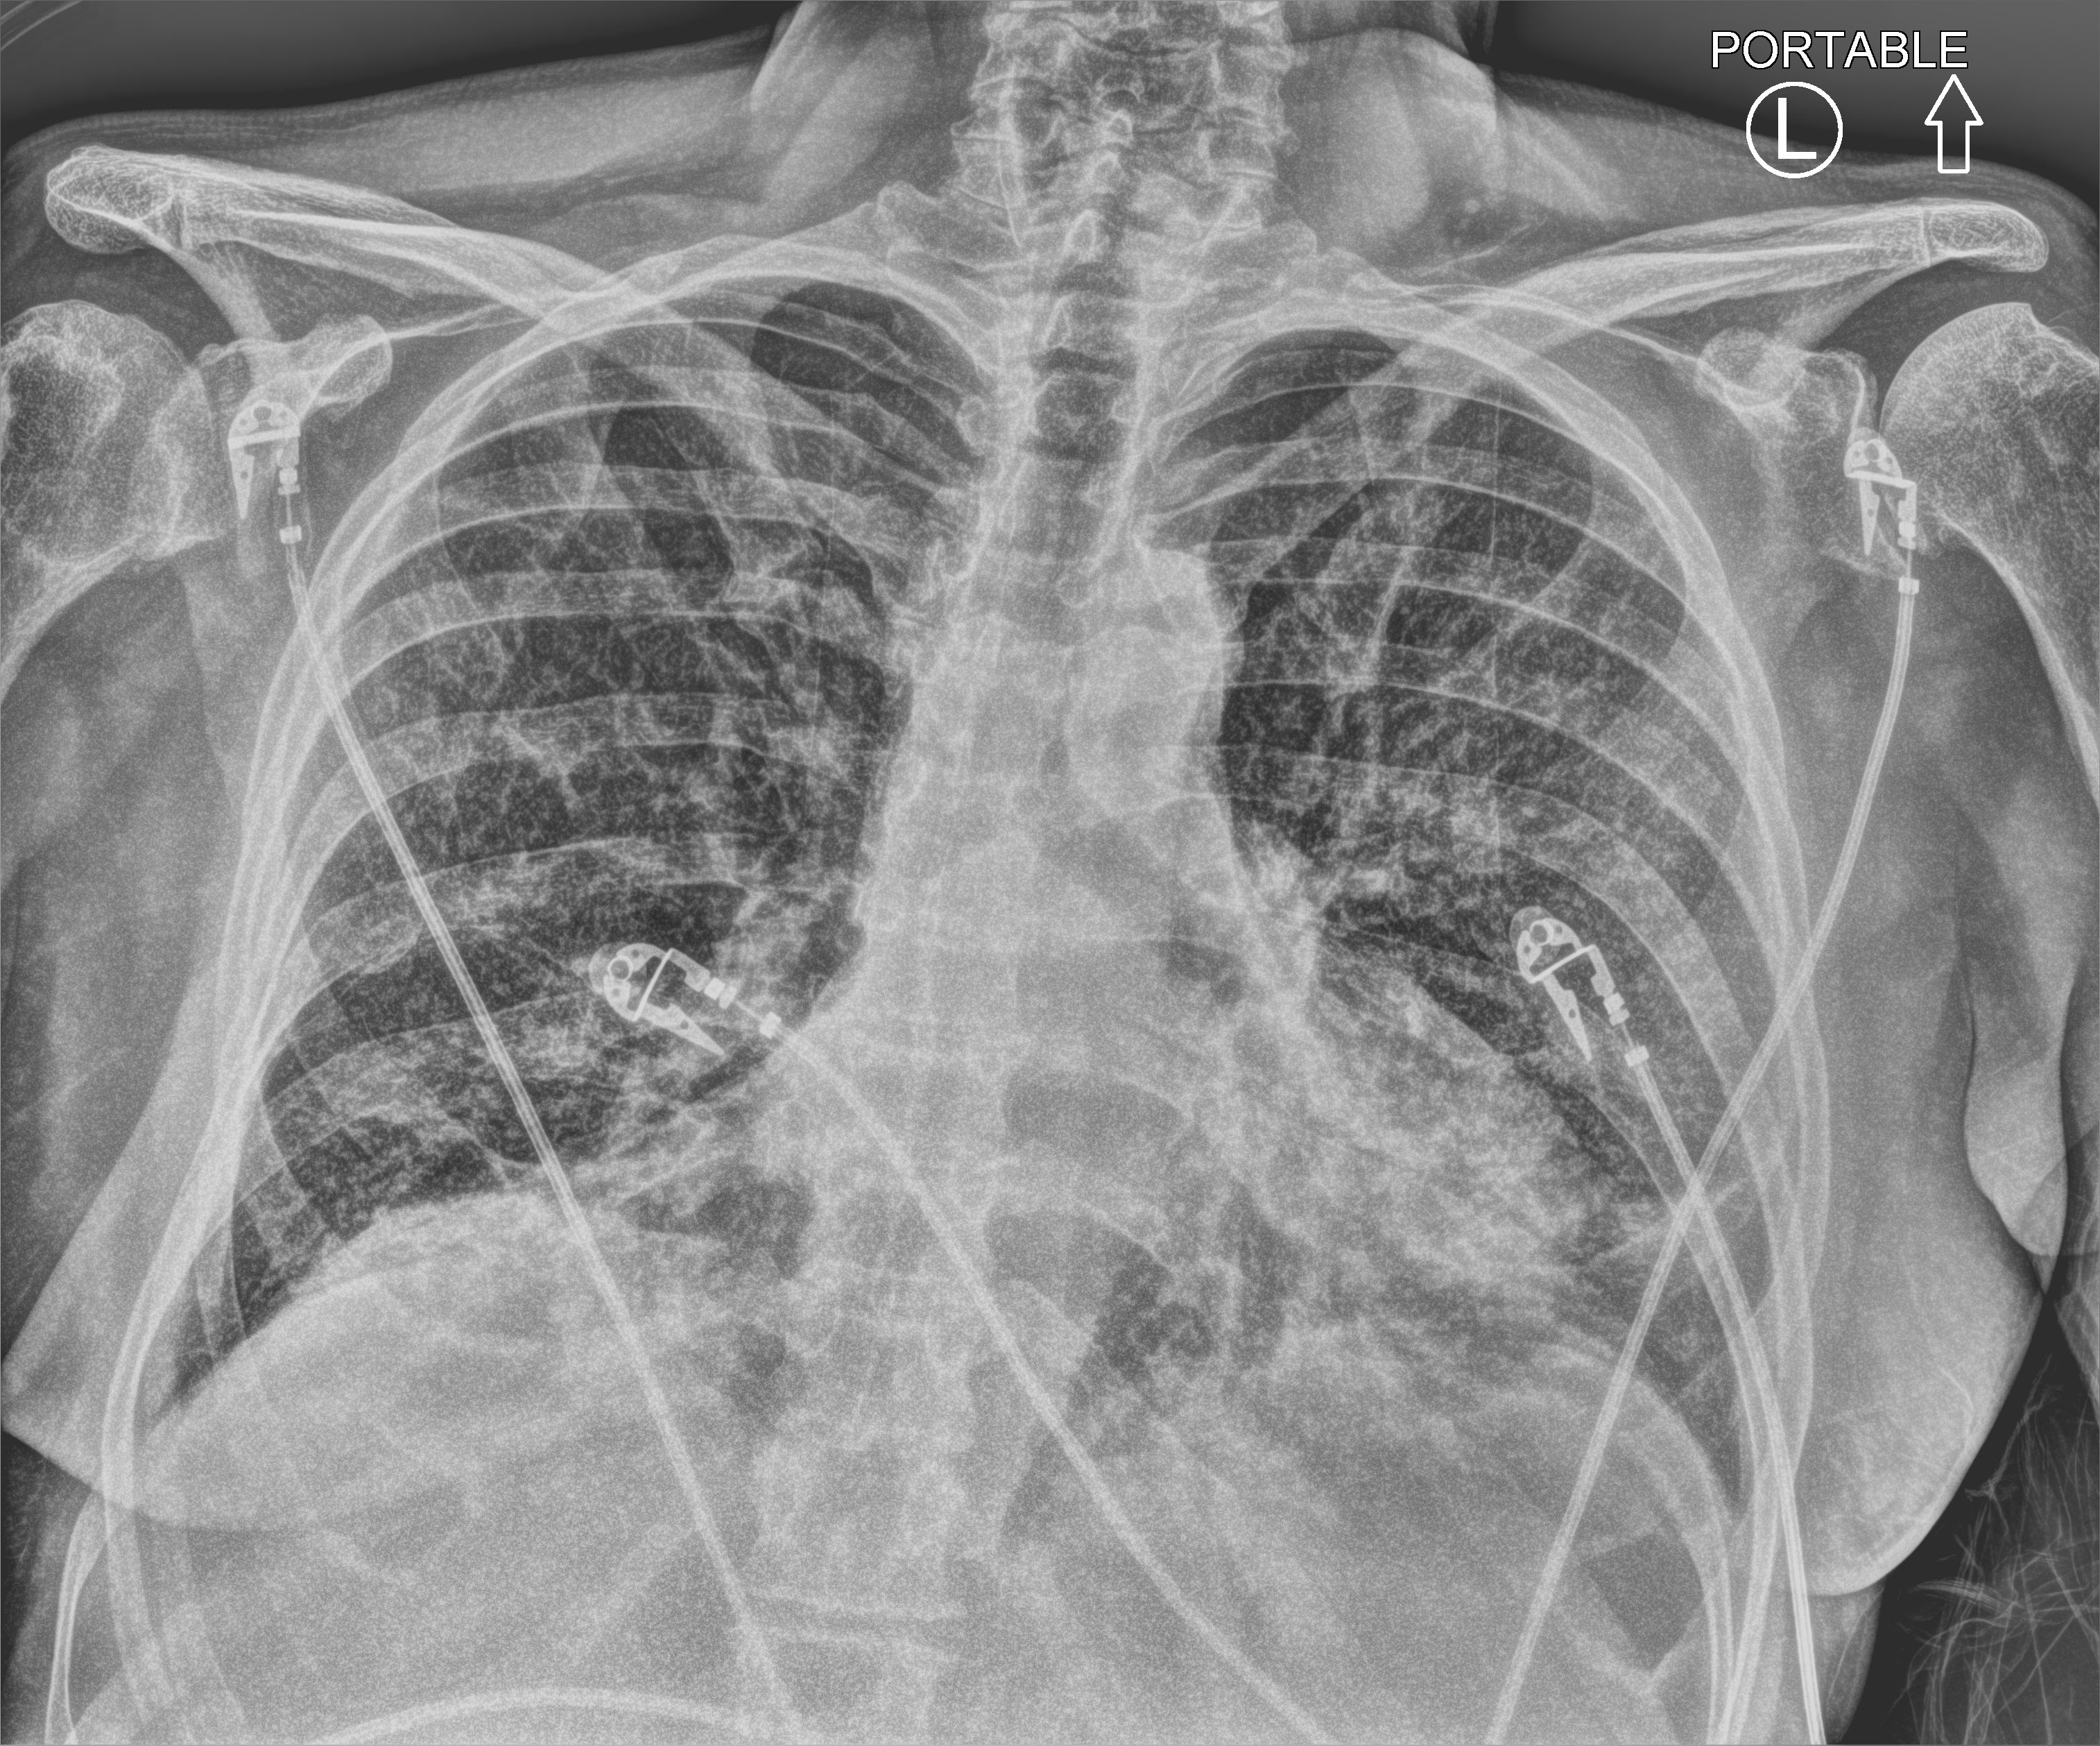
Chest X-ray (portable), anteroposterior (AP) projection. Patient hospitalised with COVID-19; male, aged 60–74 years.
Hospital-stay facts (about this admission, not read from this image; timing relative to this image not recorded):
- length of hospital stay: 15 days